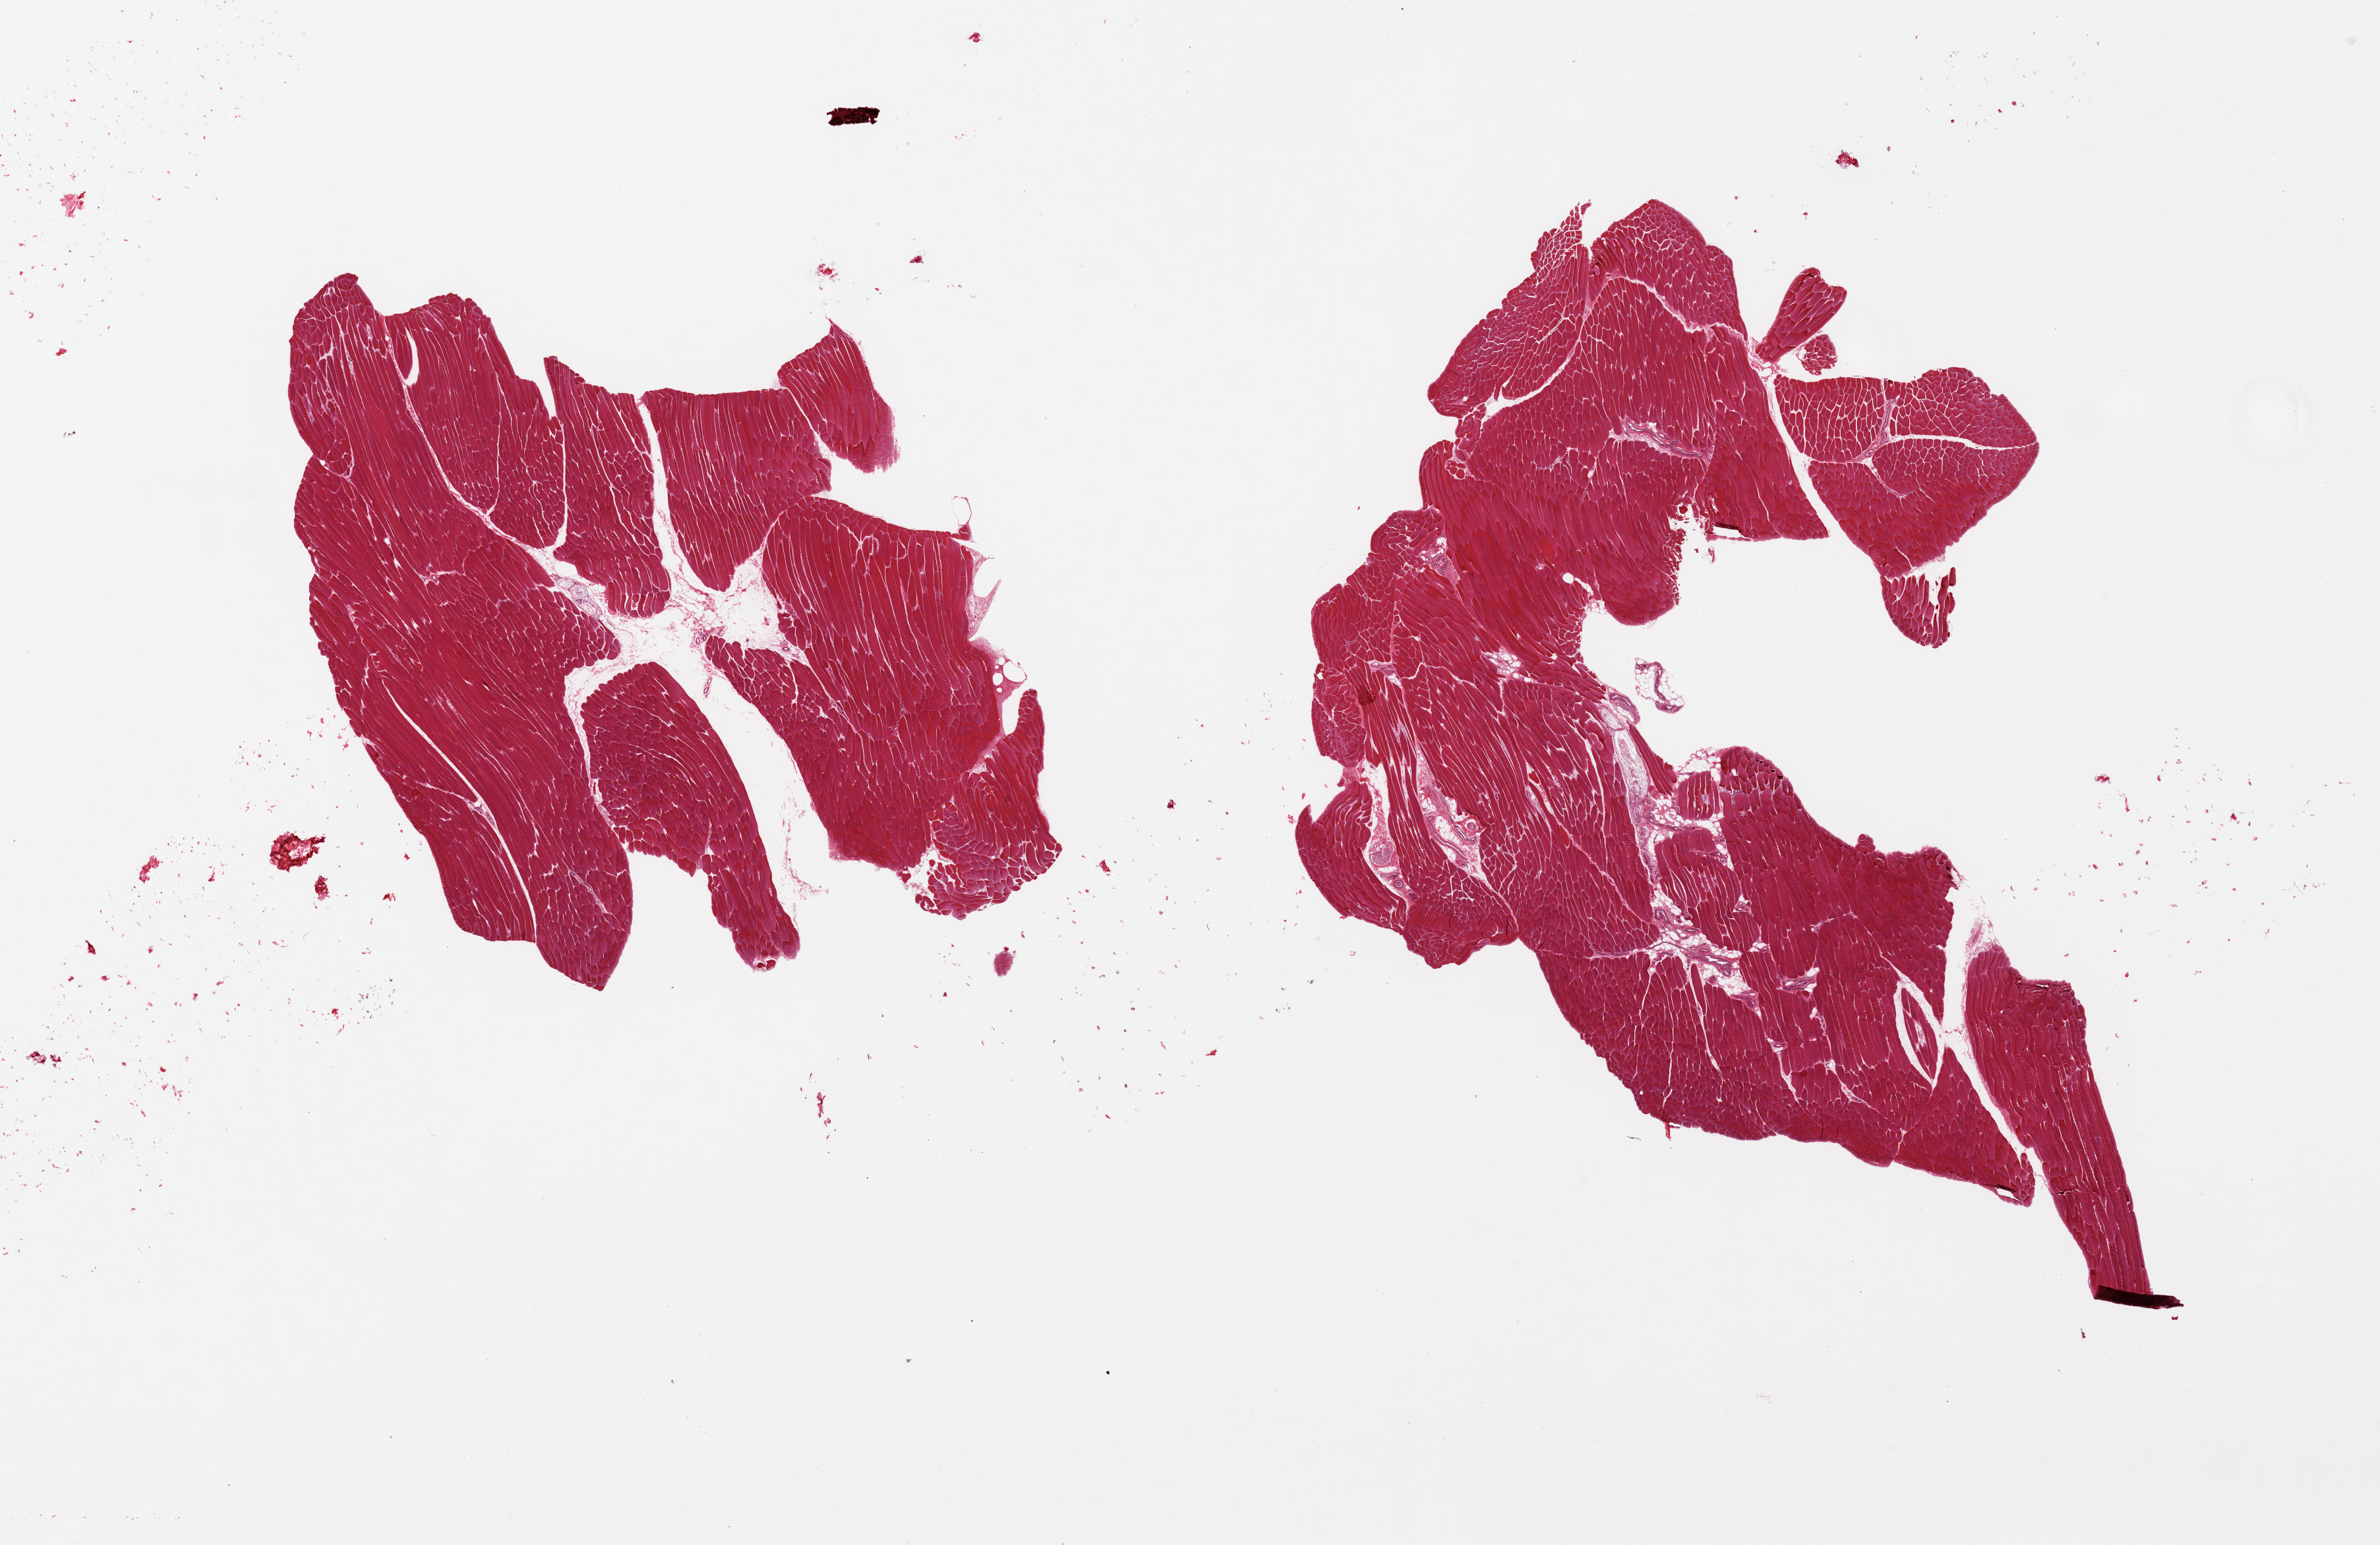
Digitized hematoxylin and eosin (H&E)-stained section, brightfield — a low-resolution overview of the entire scanned area, about 28.5 x 18.5 mm, PAXgene-fixed, paraffin-embedded tissue, section of skeletal muscle (target tissue), donor tissue sample.
Reviewer comment on this tissue sample: 2 pieces, ~10% interstitial fat/vessels; incident Pascinian corpuscle noted.